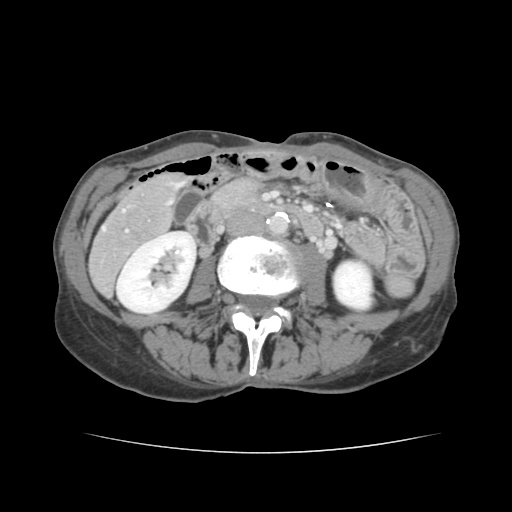
Contrast-enhanced abdominal CT, one axial slice. Slice 39 of 136 in the series (ordered by position). 120 kVp. Intravenous contrast given. Soft-tissue window (W 400 / L 40 HU). 2.5 mm slice thickness. 512 × 512 image matrix. Female patient, age 77 years. Case-level facts recorded for this patient, not image findings: diagnosis: colorectal cancer liver metastases, imaged before liver resection; multiple liver metastases: yes; largest metastasis: 3 cm; disease in both lobes: no.
Outlined on this slice (manually delineated by an expert):
- hepatic veins: bounding box <103,184,178,230> (left, top, right, bottom; pixels)
- liver: <90,175,182,293>
- portal vein (with intrahepatic branches): <126,183,176,232>